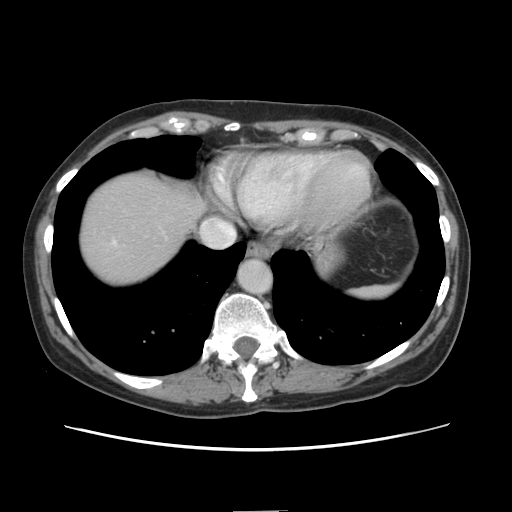
Contrast-enhanced abdominal CT, one axial slice. Slice 127 of 141 in the series (ordered by position). 120 kVp. Intravenous contrast given. Soft-tissue window (W 400 / L 40 HU). 2.5 mm slice thickness. 512 × 512 image matrix, field of view 350 × 350 mm. Female patient, age 63 years. From the clinical record (not read from this slice): diagnosis: colorectal cancer liver metastases, imaged before liver resection; multiple liver metastases: yes.
Annotated regions visible in this slice (outlined manually by an expert reader):
- liver: bounding box [x1, y1, x2, y2] px = [78, 168, 201, 287]